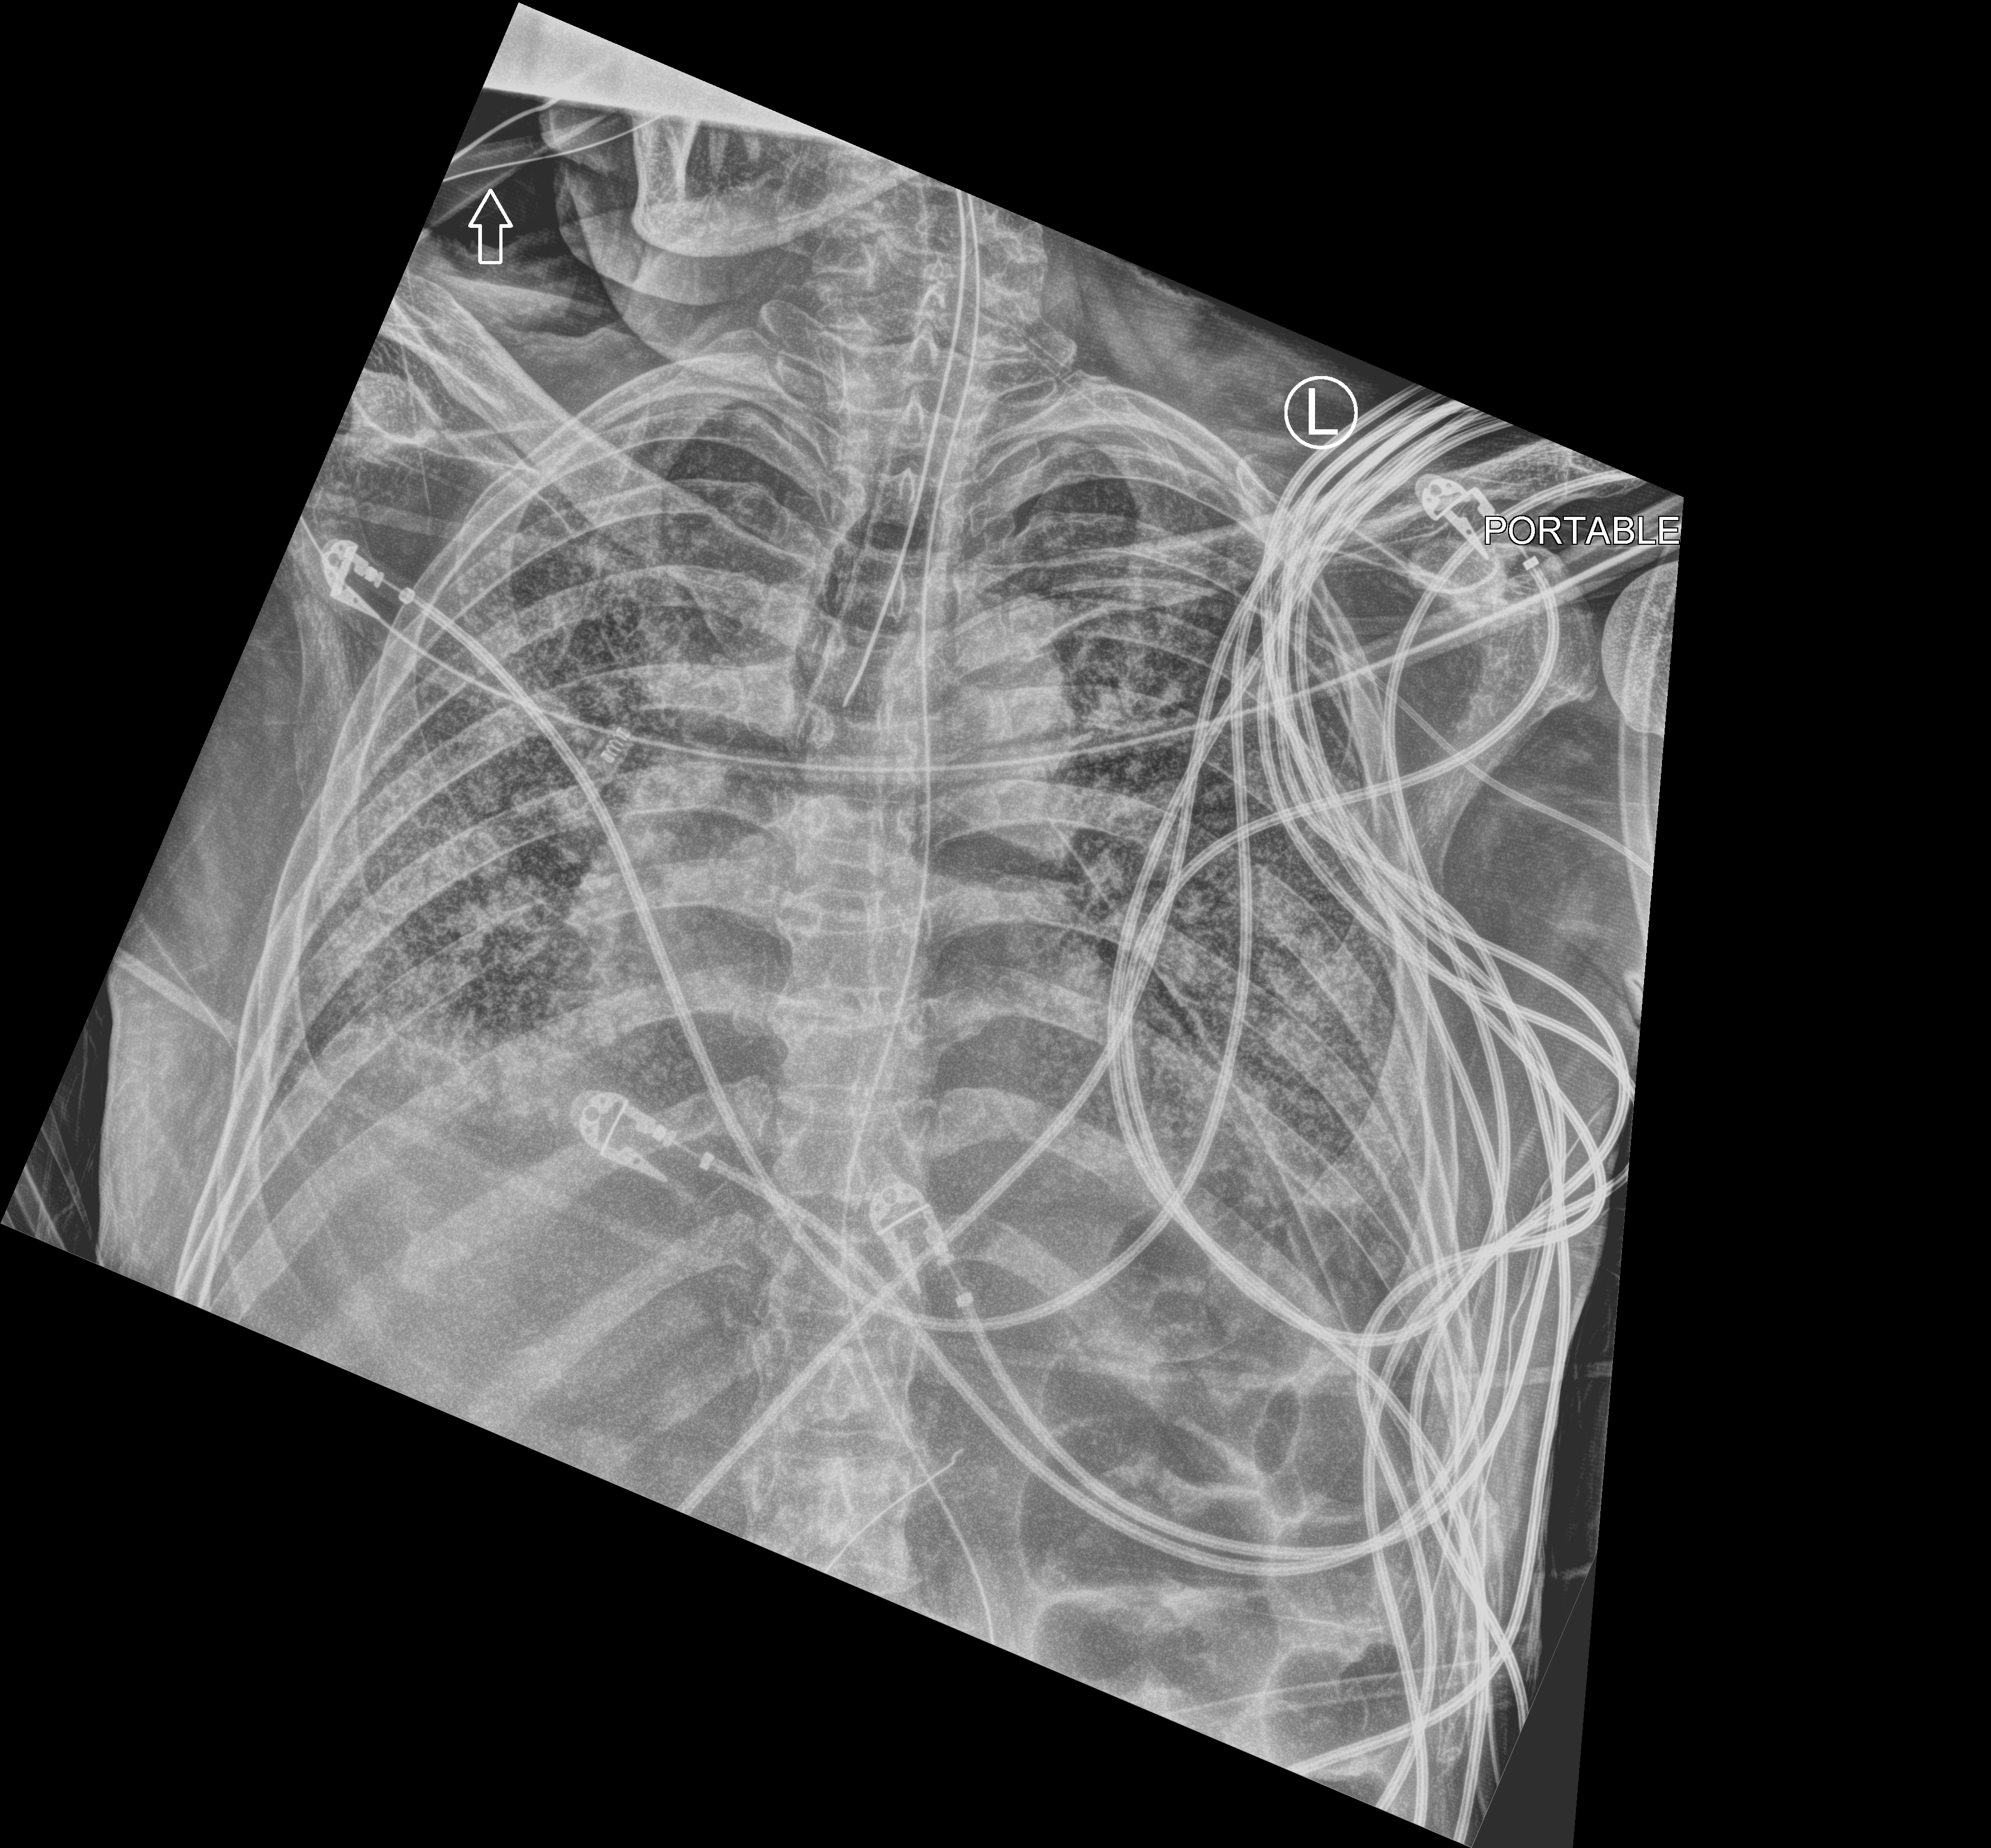
Bedside chest radiograph (computed radiography), anteroposterior (AP) projection. Patient hospitalised with COVID-19; male, aged 60–74 years.
Hospital-stay facts (about this admission, not read from this image; timing relative to this image not recorded): length of hospital stay: 54 days; admitted to intensive care during this hospital stay: yes; mechanically ventilated during this hospital stay: yes.